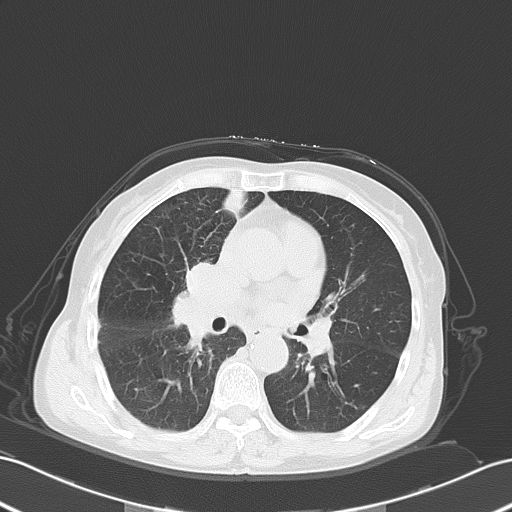
Chest CT, one axial slice; position 29 of 55 along the scan axis; reconstruction kernel B70f; 120 kVp; lung window (W 1500 / L -600 HU); 512 × 512 image matrix. Female patient, age 67 years. From the clinical record (not read from this slice): clinical TNM (as recorded): T2a N3 M0.
Outlined on this slice (bounding box drawn by a radiologist):
- lung tumour (recorded histology: small cell carcinoma): bounding box <164,254,223,339> (left, top, right, bottom; pixels)